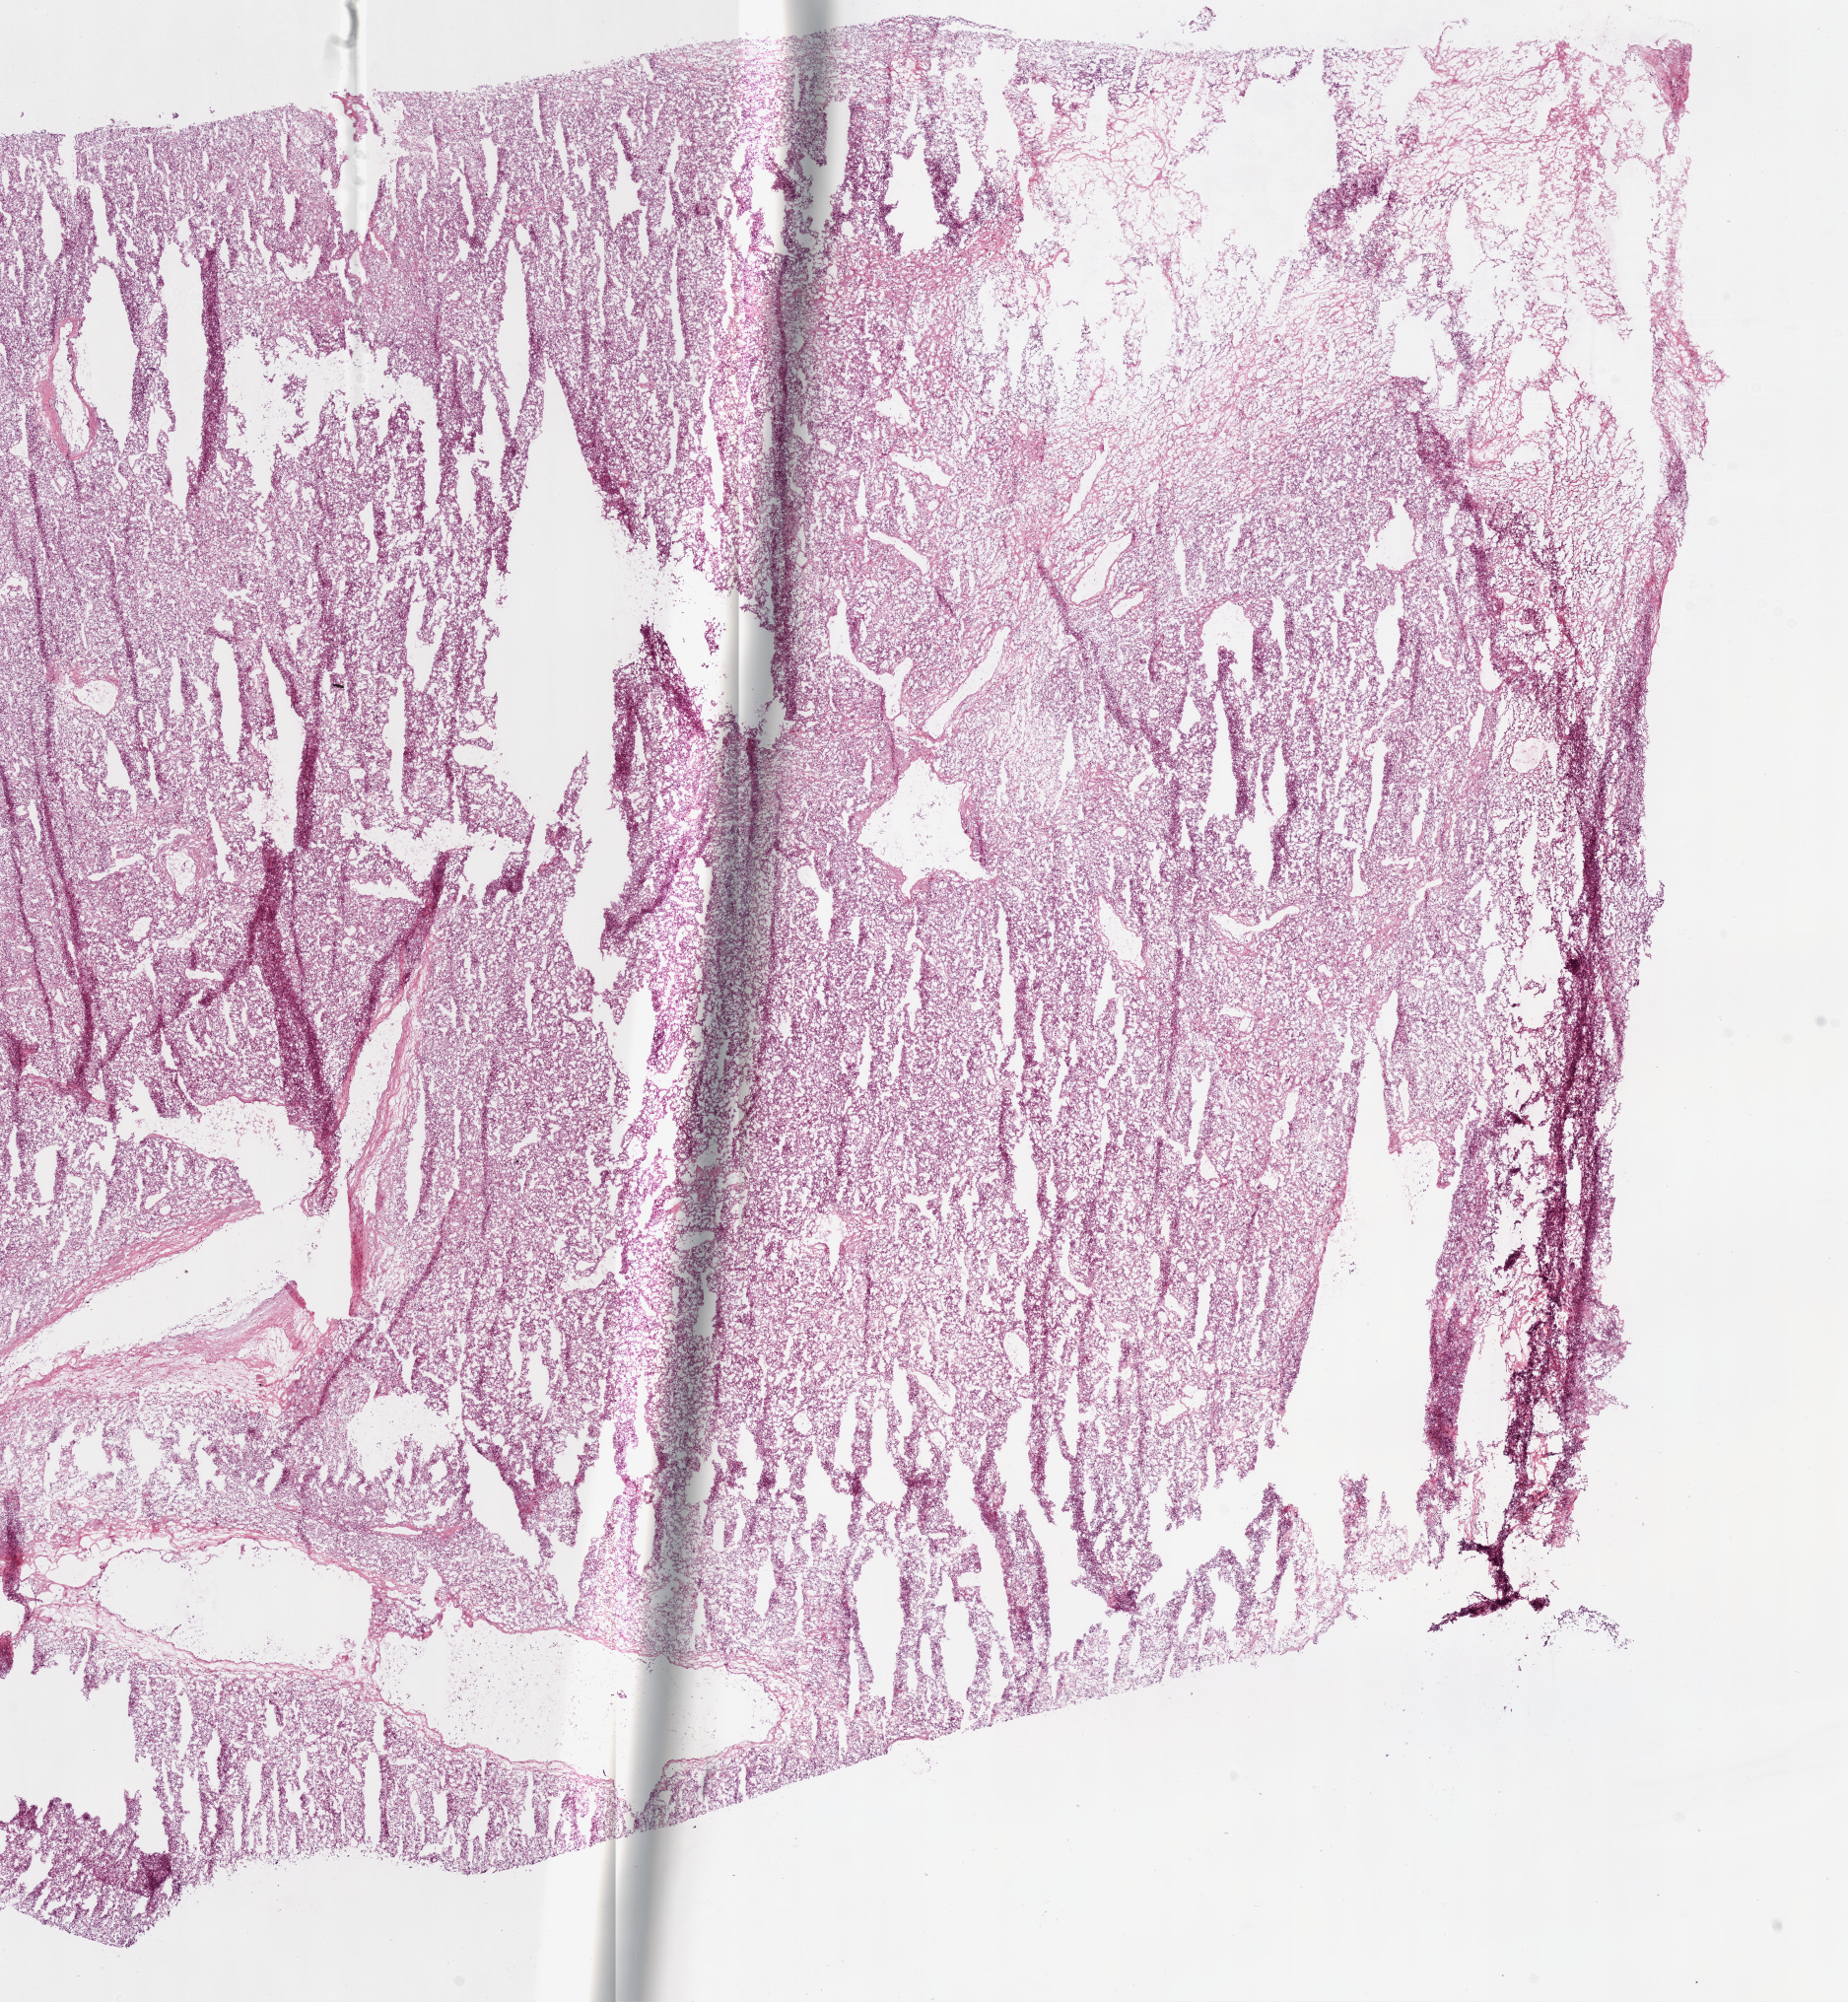
Digitized H&E-stained tissue section (whole slide) — a low-resolution overview of the entire scanned area, about 15.0 x 16.3 mm (slide scanned at 20x), frozen section, primary tumour sample from the kidney. Female, age 75 years at initial diagnosis. Histologic grade: G3 (poorly differentiated). Pathologist review of this section (percent, as recorded): tumour cells 90%, tumour nuclei 85%, normal cells 0%, stromal cells 10%, necrosis 0%.
• histologic diagnosis: Clear cell adenocarcinoma, NOS
• AJCC pathologic stage: III